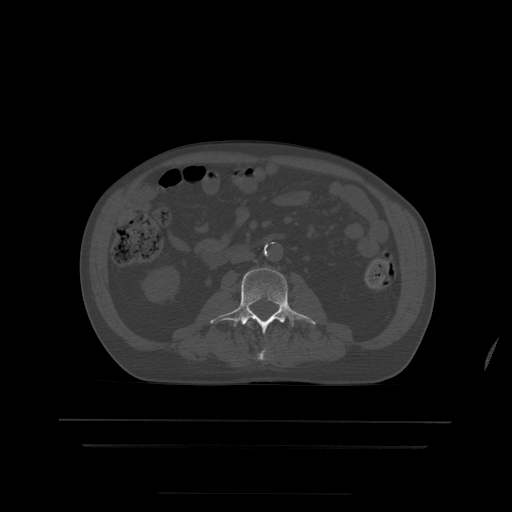
CT including the spine, one axial slice; bone window (W 1800 / L 400 HU); 512 × 512 image matrix, field of view 436 × 436 mm. Patient age 68 years. Case-level facts recorded for this patient, not image findings: primary cancer: urothelial.
Structures marked on this image (semi-automatically segmented with operator editing):
- L2 vertebra: box from (x=244, y=322) to (x=266, y=361) px
- L3 vertebra: (x=210, y=268)–(x=316, y=334)